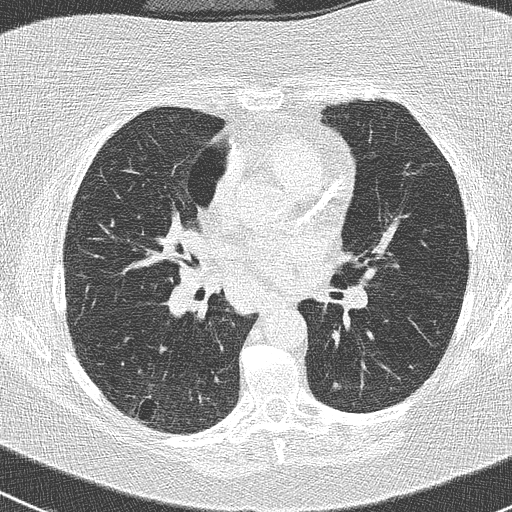
Low-dose screening chest CT, one axial slice. Slice 134 of 261 in the series (ordered by position). Reconstruction kernel B50f. 120 kVp. Lung window (W 1500 / L -600 HU). 512 × 512 image matrix, field of view 310 × 310 mm.
Outlined on this slice (outlined manually by an expert reader):
- lesion 1 (tumor, lower lobe of right lung): box from (x=147, y=395) to (x=151, y=399) px